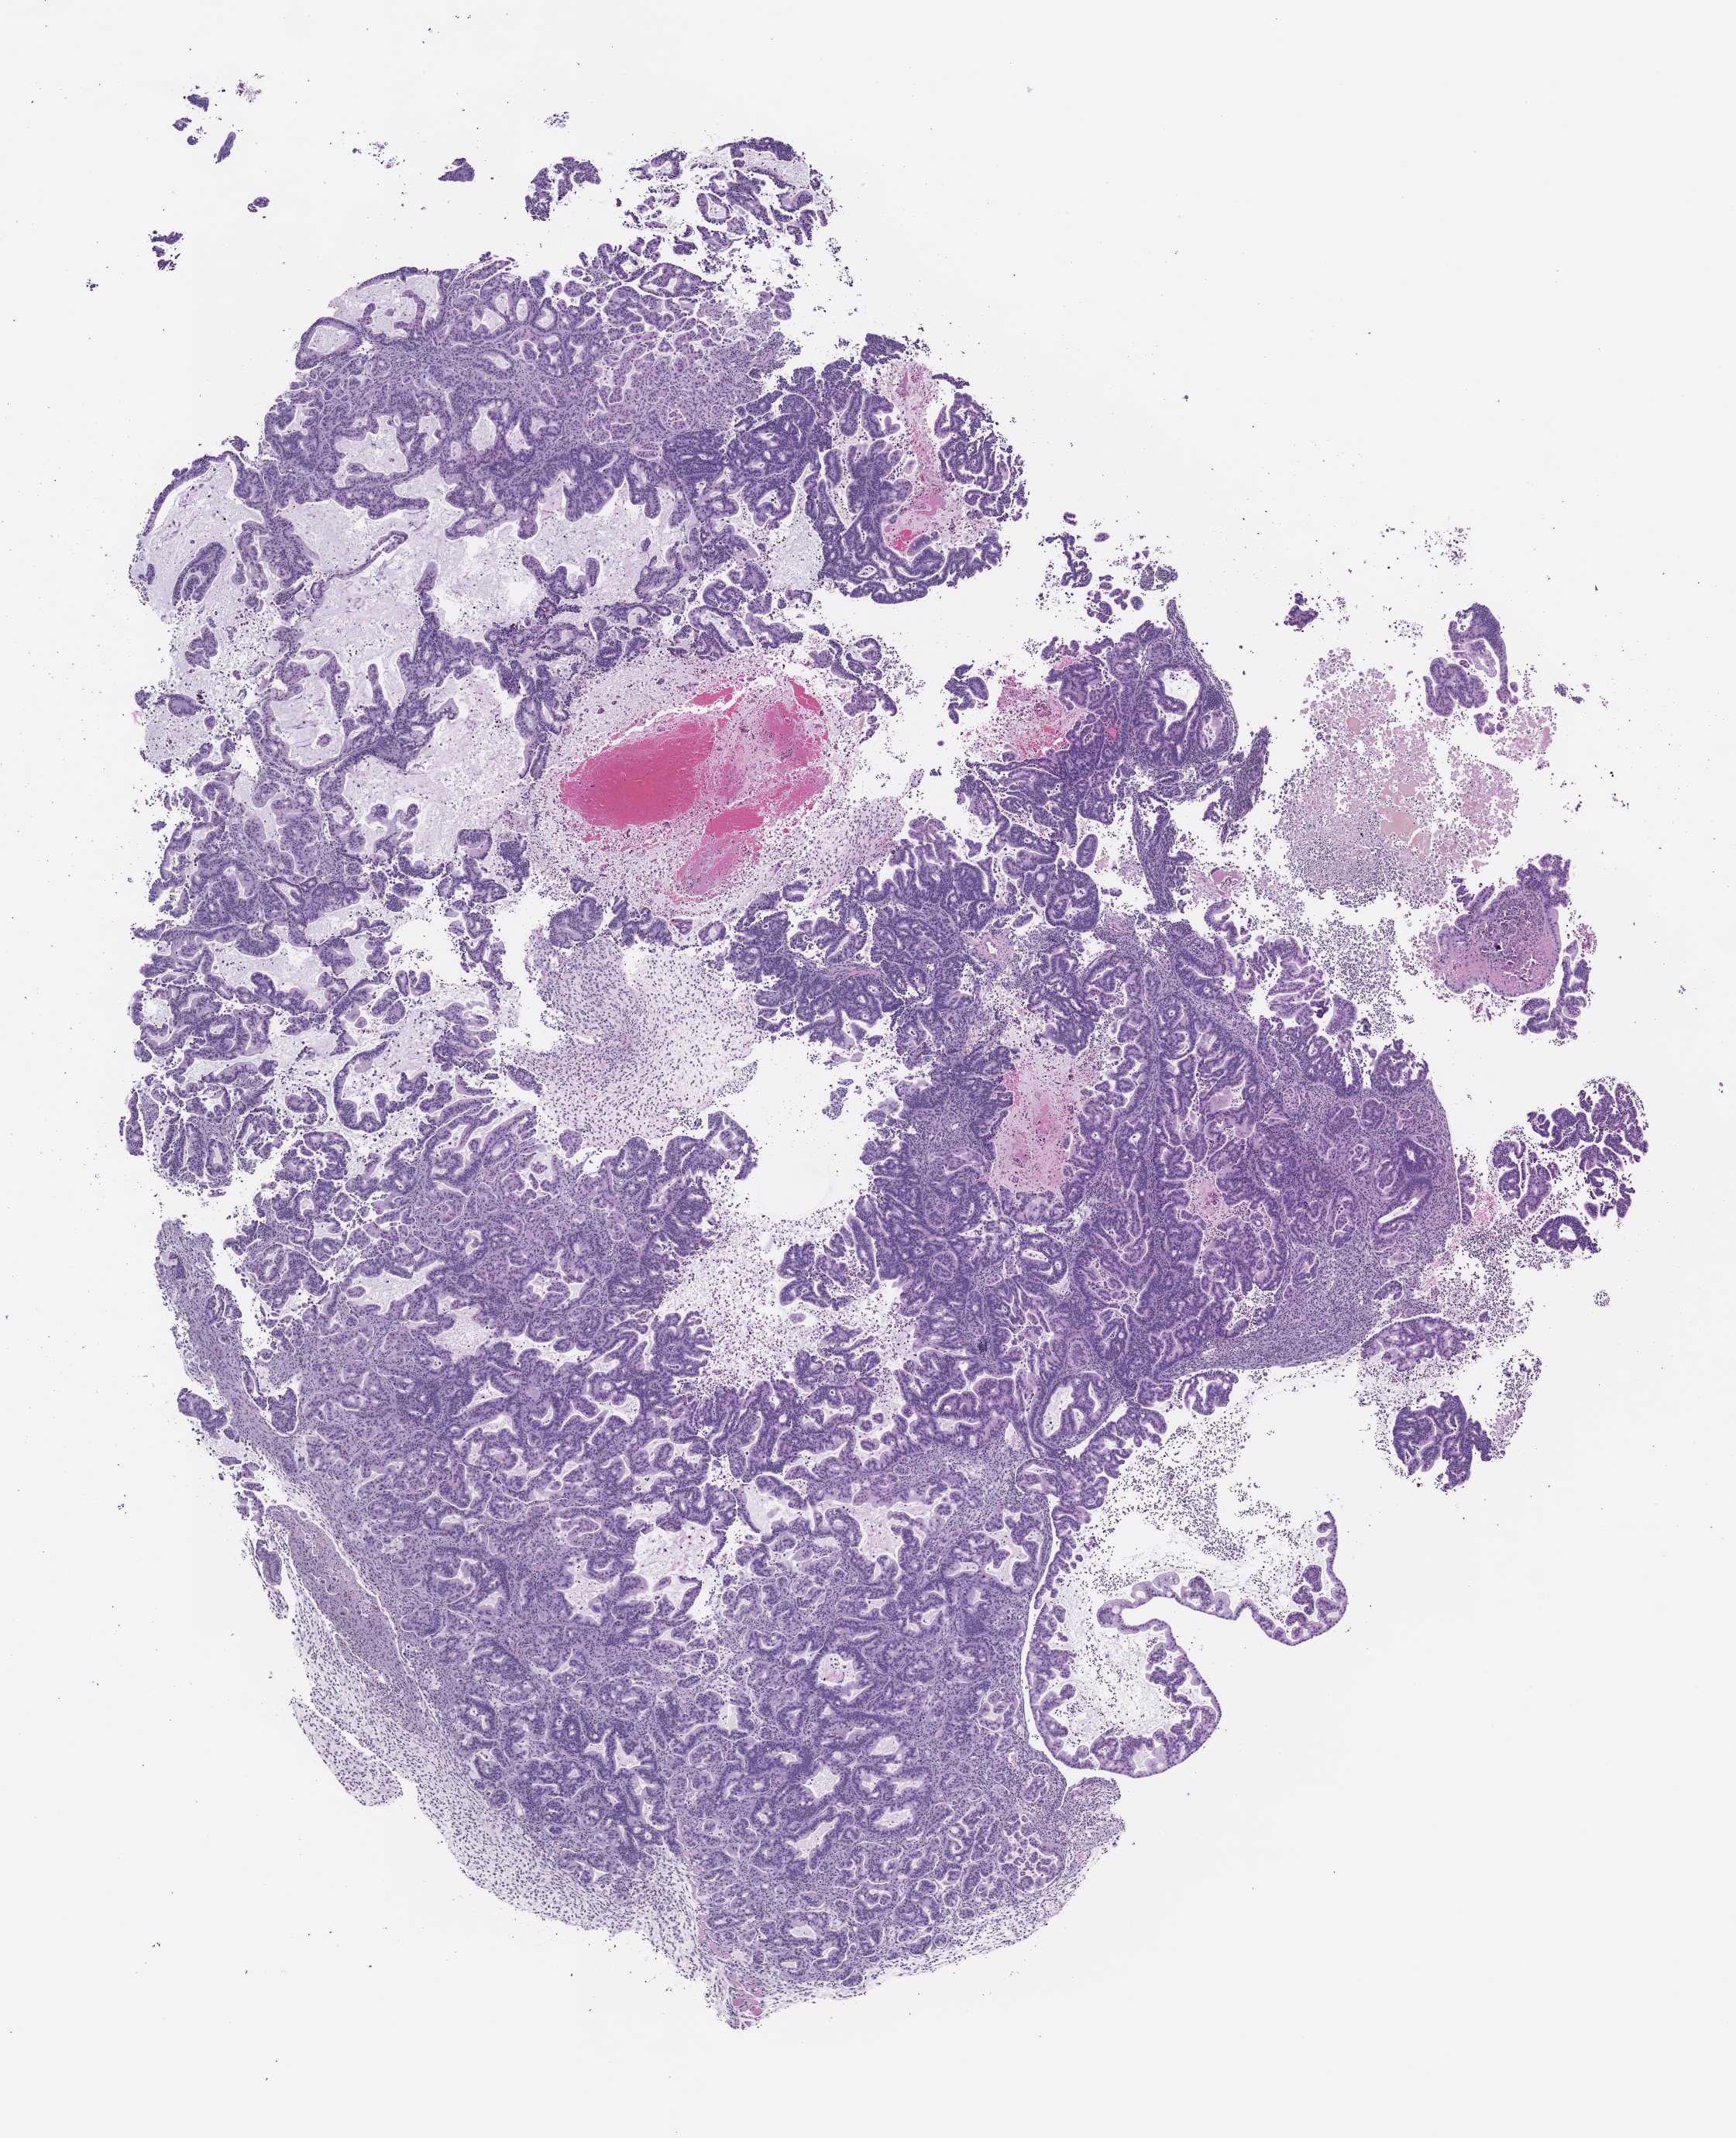
Haematoxylin and eosin whole-slide image of a patient-derived xenograft (PDX) tumor grown in a mouse, passage 1, shown as a low-resolution overview of the whole scanned area (about 9.0 x 11.1 mm); FFPE section; tumor site category: pancreas.
• originating patient diagnosis: Pancreatic Adenocarcinoma